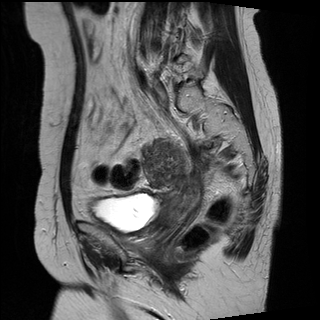
Pelvic MRI for cervical cancer, one sagittal slice; slice 9 of 27 in the series (ordered by position); T2-weighted; 1.5 T; TE 89 ms, TR 2740 ms; 320 × 320 image matrix, field of view 260 × 260 mm. Female patient, age 42 years.
Structures marked on this image (outlined manually by an expert reader):
- uterus and cervix: bounding box [x1, y1, x2, y2] px = [142, 138, 202, 226]